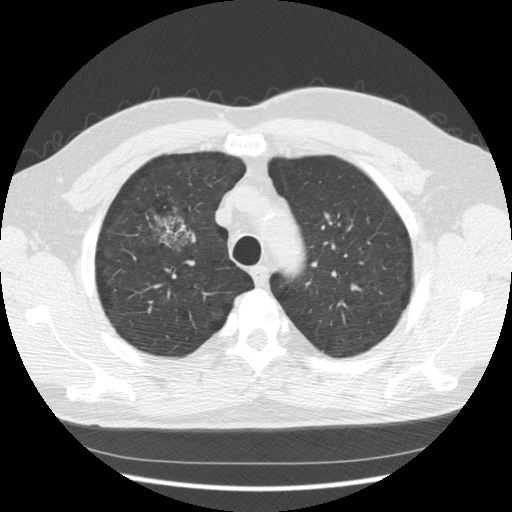
Low-dose screening chest CT, one axial slice; position 97 of 133 along the scan axis; 140 kVp; lung window (W 1500 / L -600 HU); 512 × 512 image matrix, field of view 369 × 369 mm.
Annotated regions visible in this slice (expert manual segmentation):
- lesion 1 (tumor, upper lobe of right lung): box from (x=154, y=216) to (x=190, y=248) px